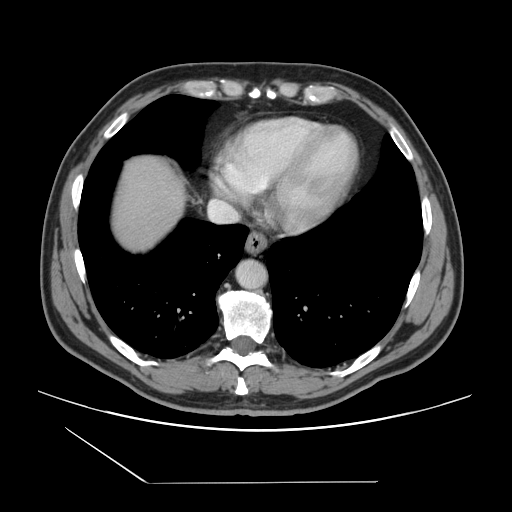
Contrast-enhanced abdominal CT, one axial slice; intravenous contrast given; soft-tissue window (W 400 / L 40 HU); 512 × 512 image matrix, field of view 407 × 407 mm. Male patient, age 61 years. Case-level facts recorded for this patient, not image findings: diagnosis: colorectal cancer liver metastases, imaged before liver resection; multiple liver metastases: yes; largest metastasis: 5.5 cm; disease in both lobes: yes.
Structures marked on this image (outlined manually by an expert reader):
- liver: box from (x=114, y=159) to (x=184, y=246) px
- planned liver remnant (the part of the liver to remain after resection): (x=114, y=160)–(x=183, y=229)